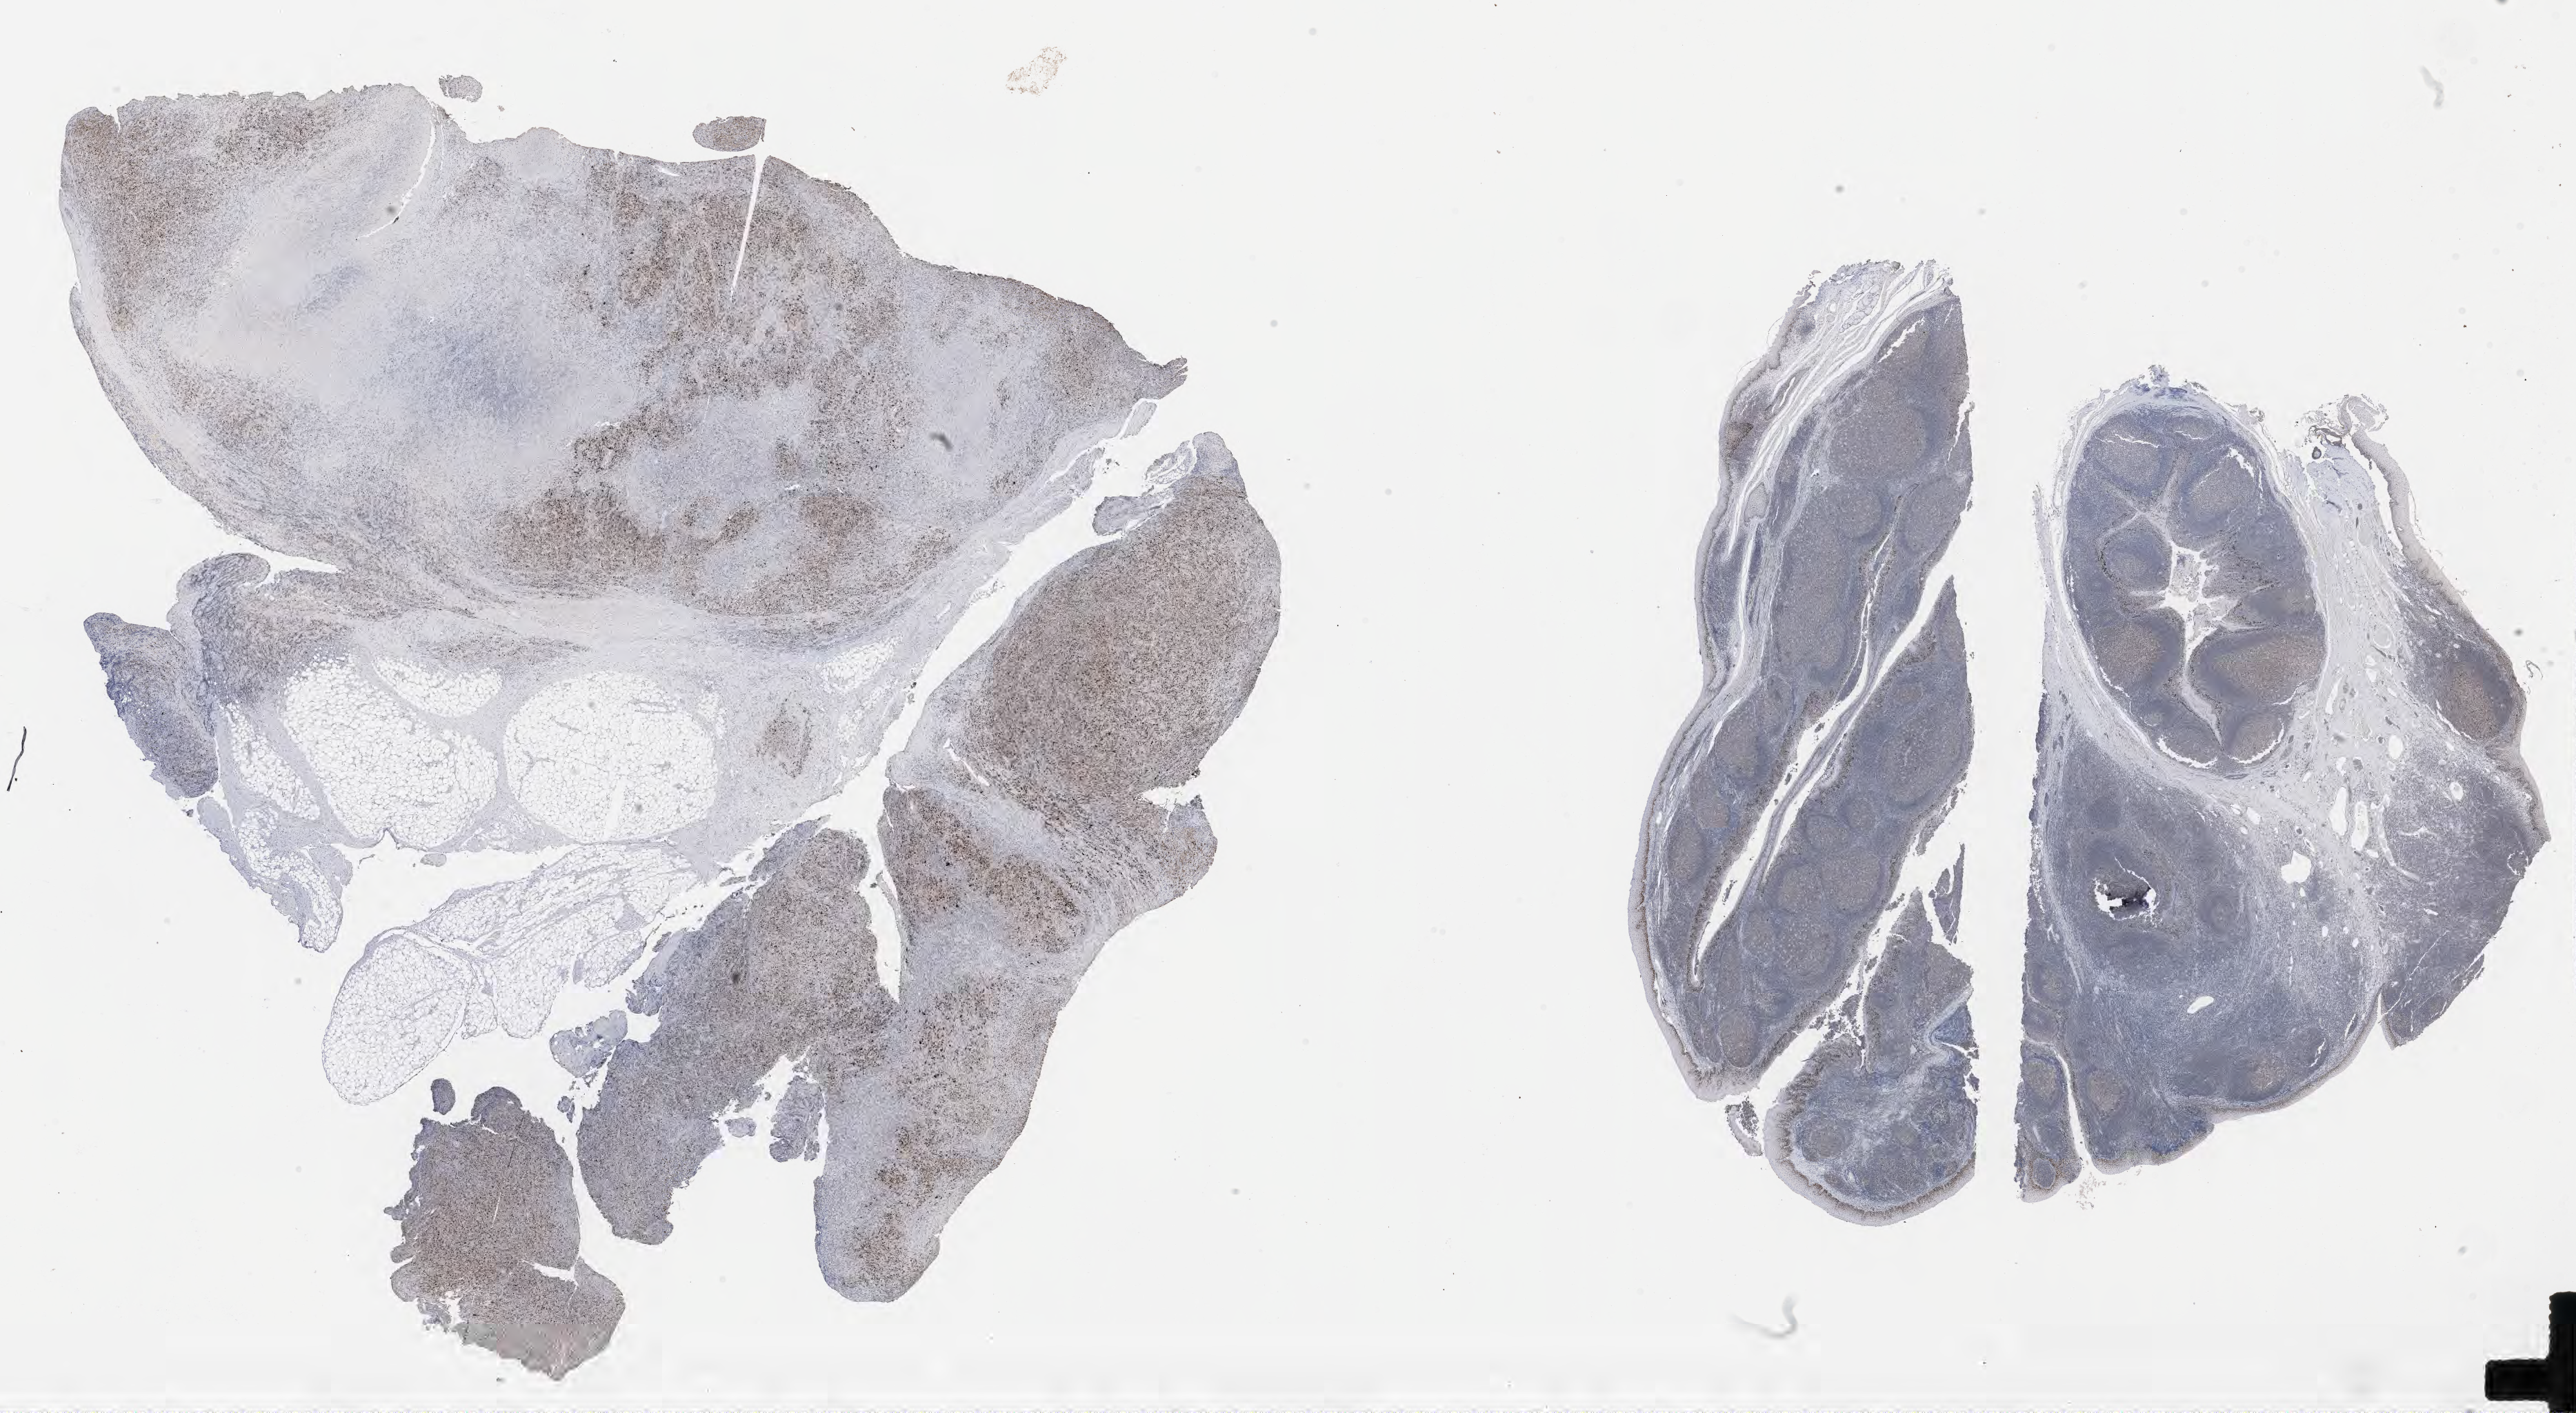
IHC for p53, whole-slide image — whole scanned area (about 30.2 x 16.6 mm) shown as a low-resolution overview. Specimen: tumor tissue. Patient female; aged 46.
- diagnosis: Diffuse large B-cell lymphoma, NOS